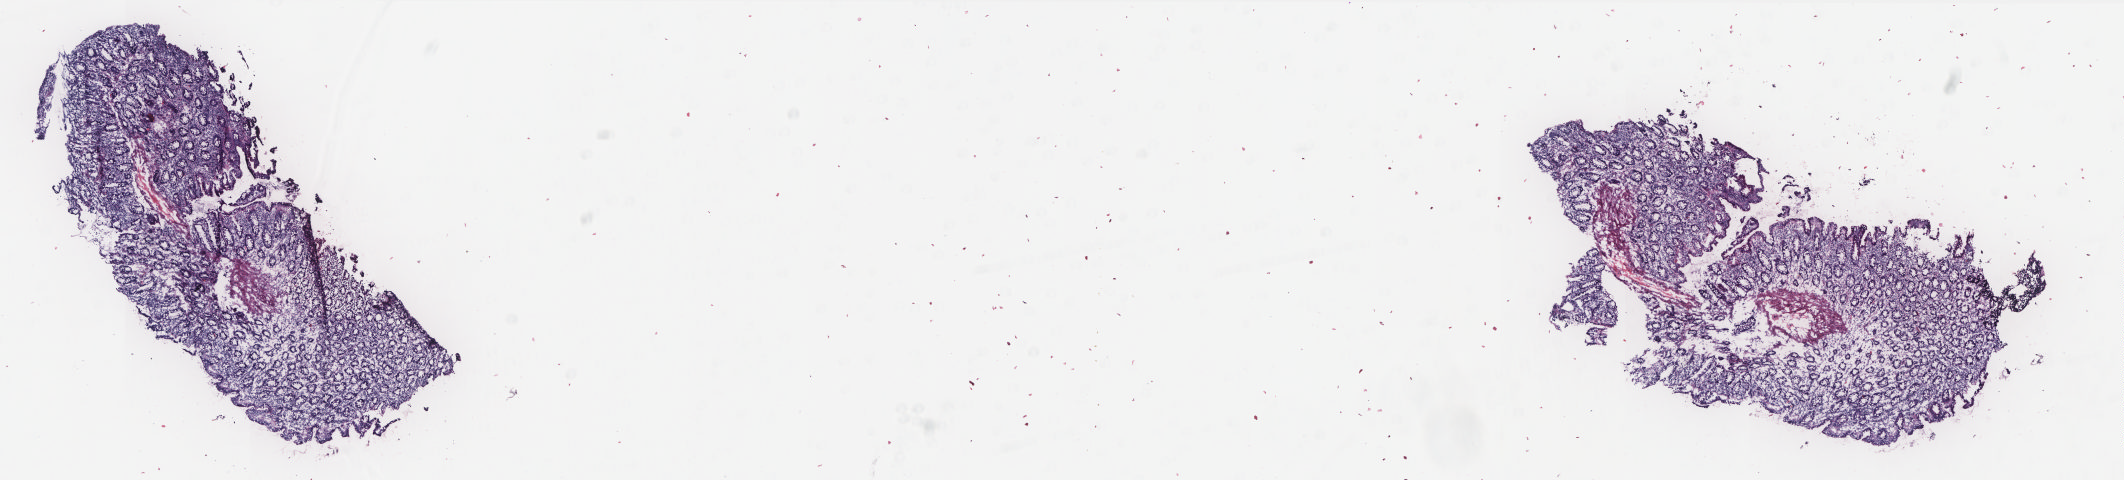
Whole-slide histology image, H&E, whole scanned area (about 17.0 x 3.8 mm, slide scanned at 20x) shown as a low-resolution overview; frozen section; solid tissue normal (non-tumour tissue) sample from the colon. Female patient; age at initial diagnosis 80 years. Slide review estimates, as recorded: tumour cells 0%, normal cells 100%. Inflammatory infiltration, as recorded: lymphocyte infiltration 45%, monocyte infiltration 10%, neutrophil infiltration 0%.
- this section: solid tissue normal sample (biorepository sample class)
- patient diagnosis: Adenocarcinoma, NOS (ascending colon)